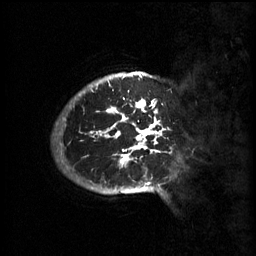
Breast MRI (dynamic contrast-enhanced), one sagittal slice. Slice 51 of 60 in the series (ordered by position). 3 images stored at this slice position (order not interpretable as contrast timing). 1.5 T. TE 4.2 ms, TR 11 ms. 2 mm slice thickness. 256 × 256 image matrix. Patient: female, 51 years.
Structures marked on this image (semi-automatic segmentation, software-assisted and operator-edited):
- analysis volume of interest (the breast-tissue region the enhancement analysis was run in; not a lesion): bounding box <63,80,179,197> (left, top, right, bottom; pixels)
- tumour enhancement mask (voxels above the 70 % enhancement threshold inside the analysis volume of interest): <91,80,165,193>